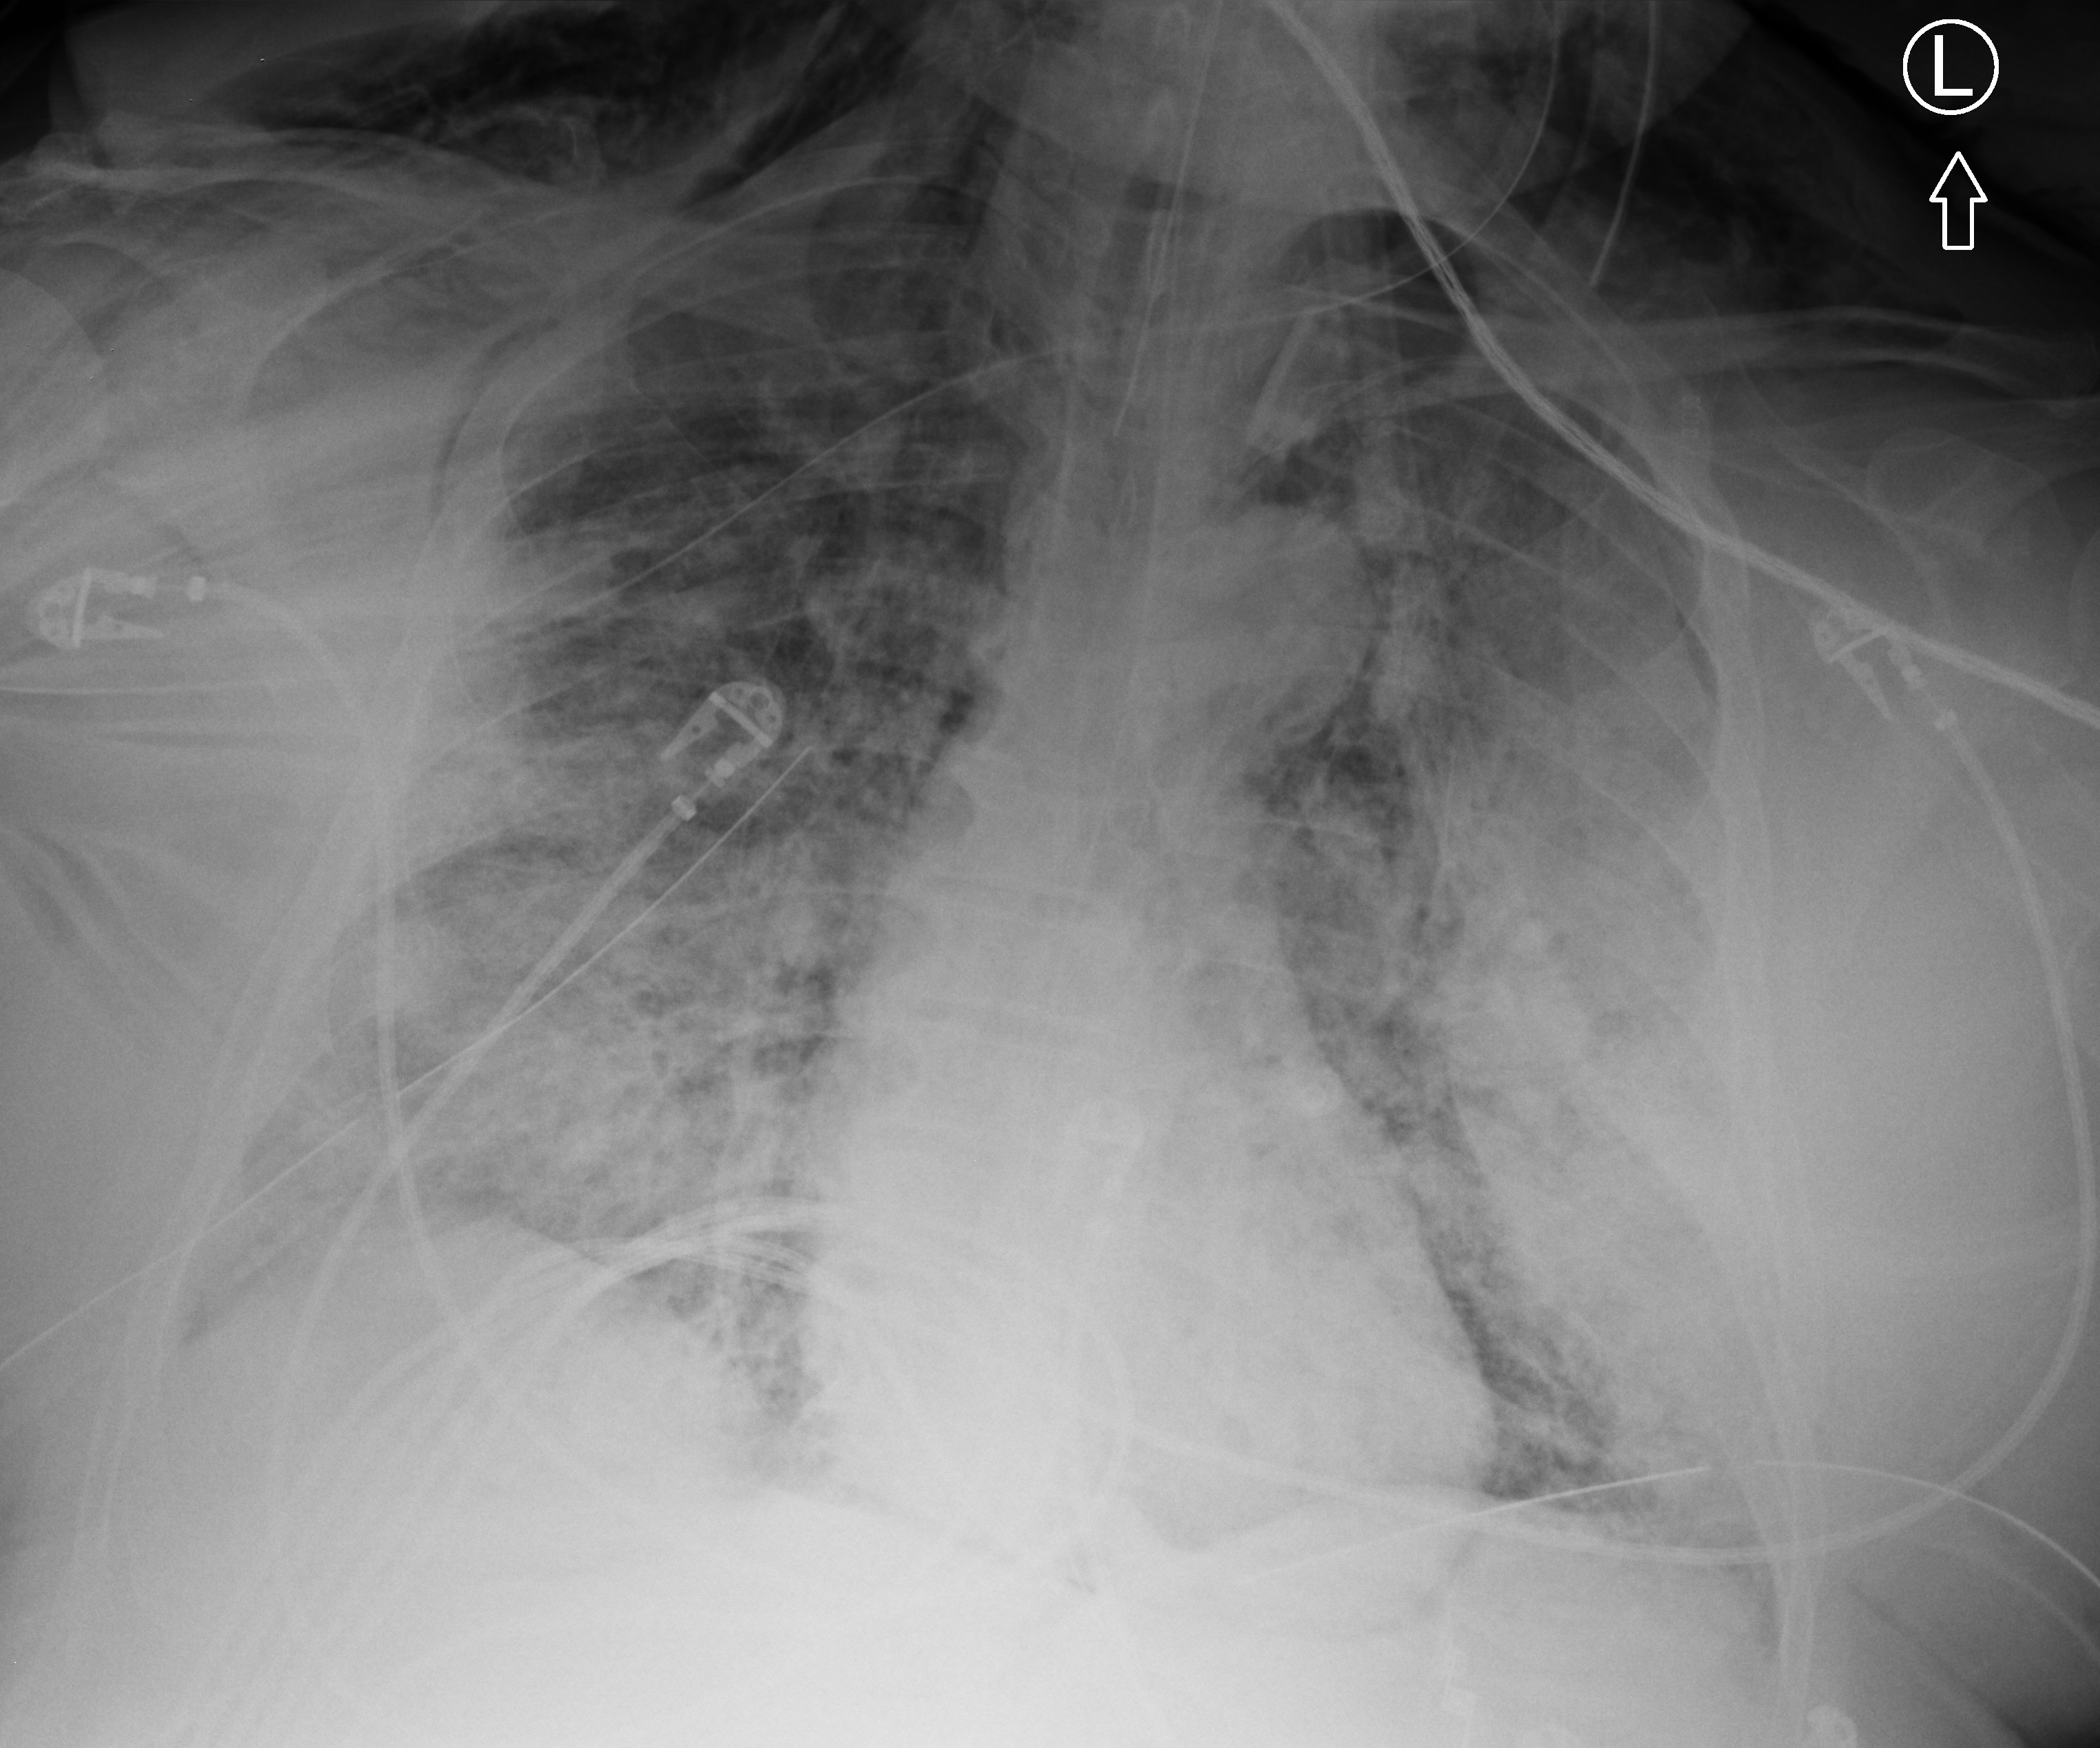
Bedside chest radiograph (computed radiography); anteroposterior (AP) projection. Adult patient hospitalised with COVID-19, age 18–59 years.
Admission-level facts for this patient (not findings on this image; timing relative to this image not recorded):
- admitted to intensive care during this hospital stay: yes
- other chronic lung disease (admission record): no